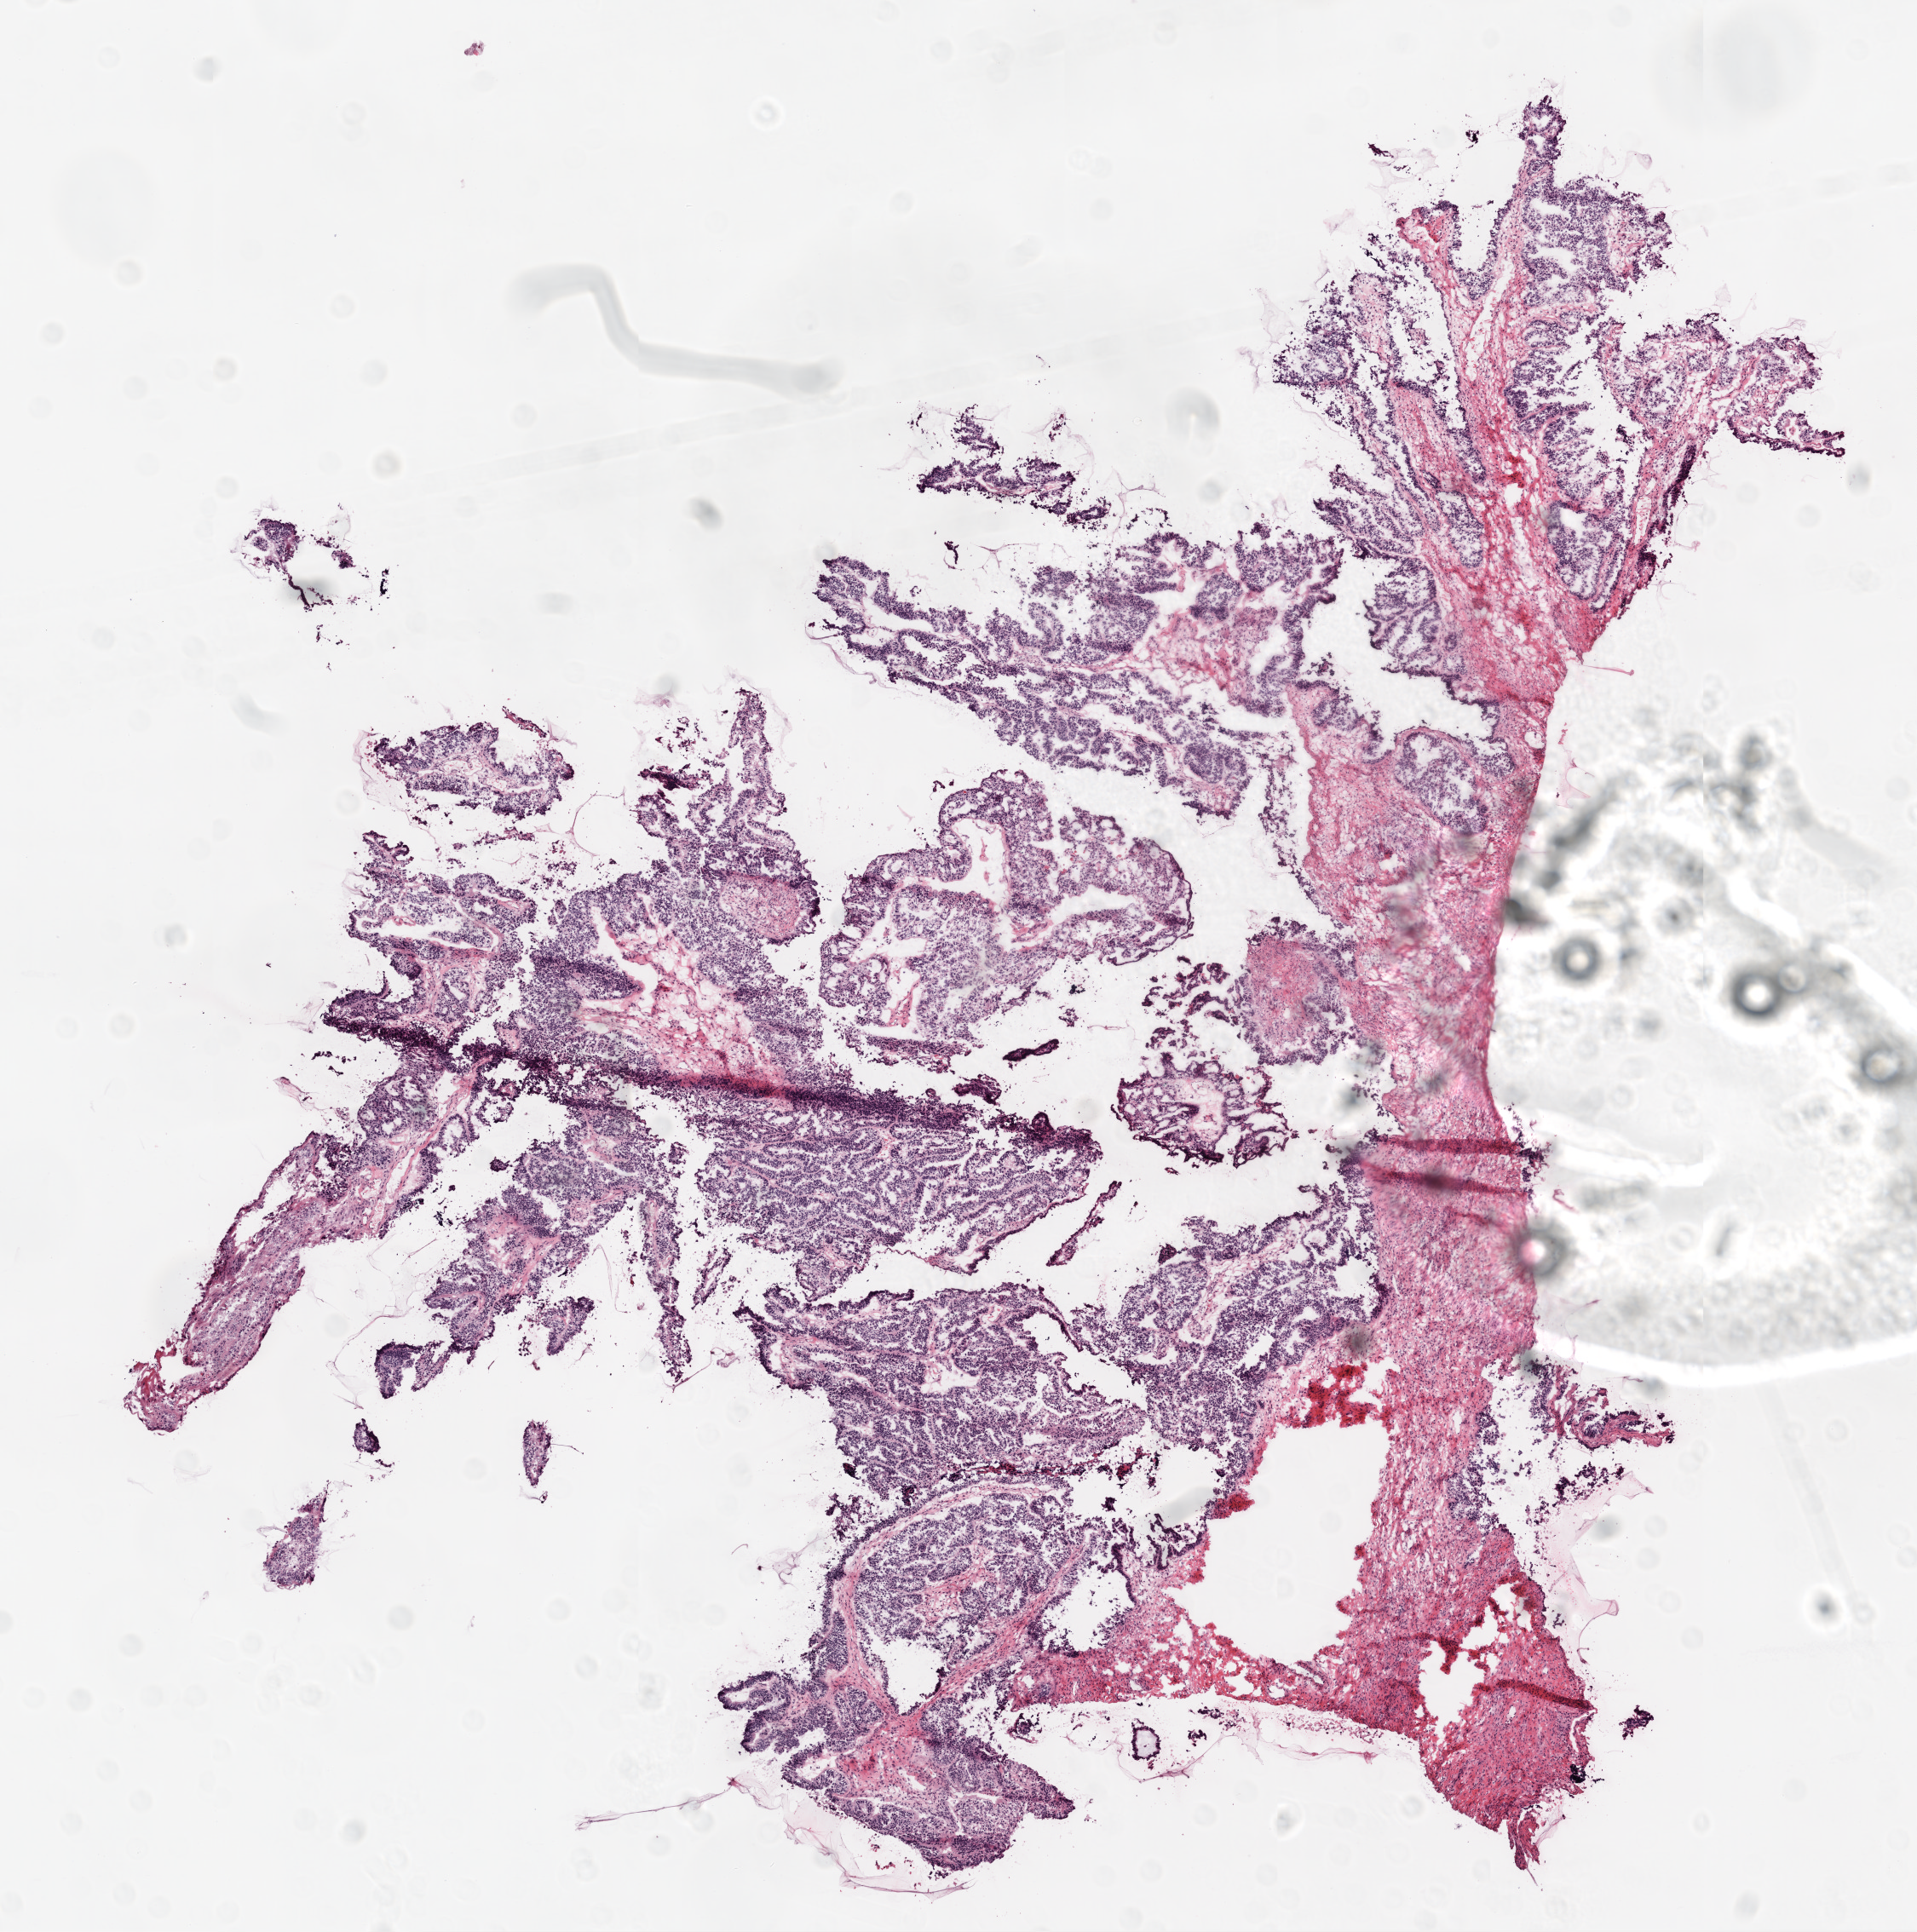
Digitized H&E tissue section (whole slide), a low-resolution overview of the entire scanned area, about 9.0 x 9.1 mm, frozen section from the top of the tissue portion, sample: primary tumour, ovary. Female, age 51 years at initial diagnosis. Histologic grade: G2 (moderately differentiated). Slide review estimates, as recorded: tumour cells 80%, tumour nuclei 85%, normal cells 0%, stromal cells 20%, necrosis 0%. Inflammatory infiltration, as recorded: lymphocyte infiltration 5%.
- pathologic diagnosis: Serous cystadenocarcinoma, NOS
- FIGO stage: IIIC